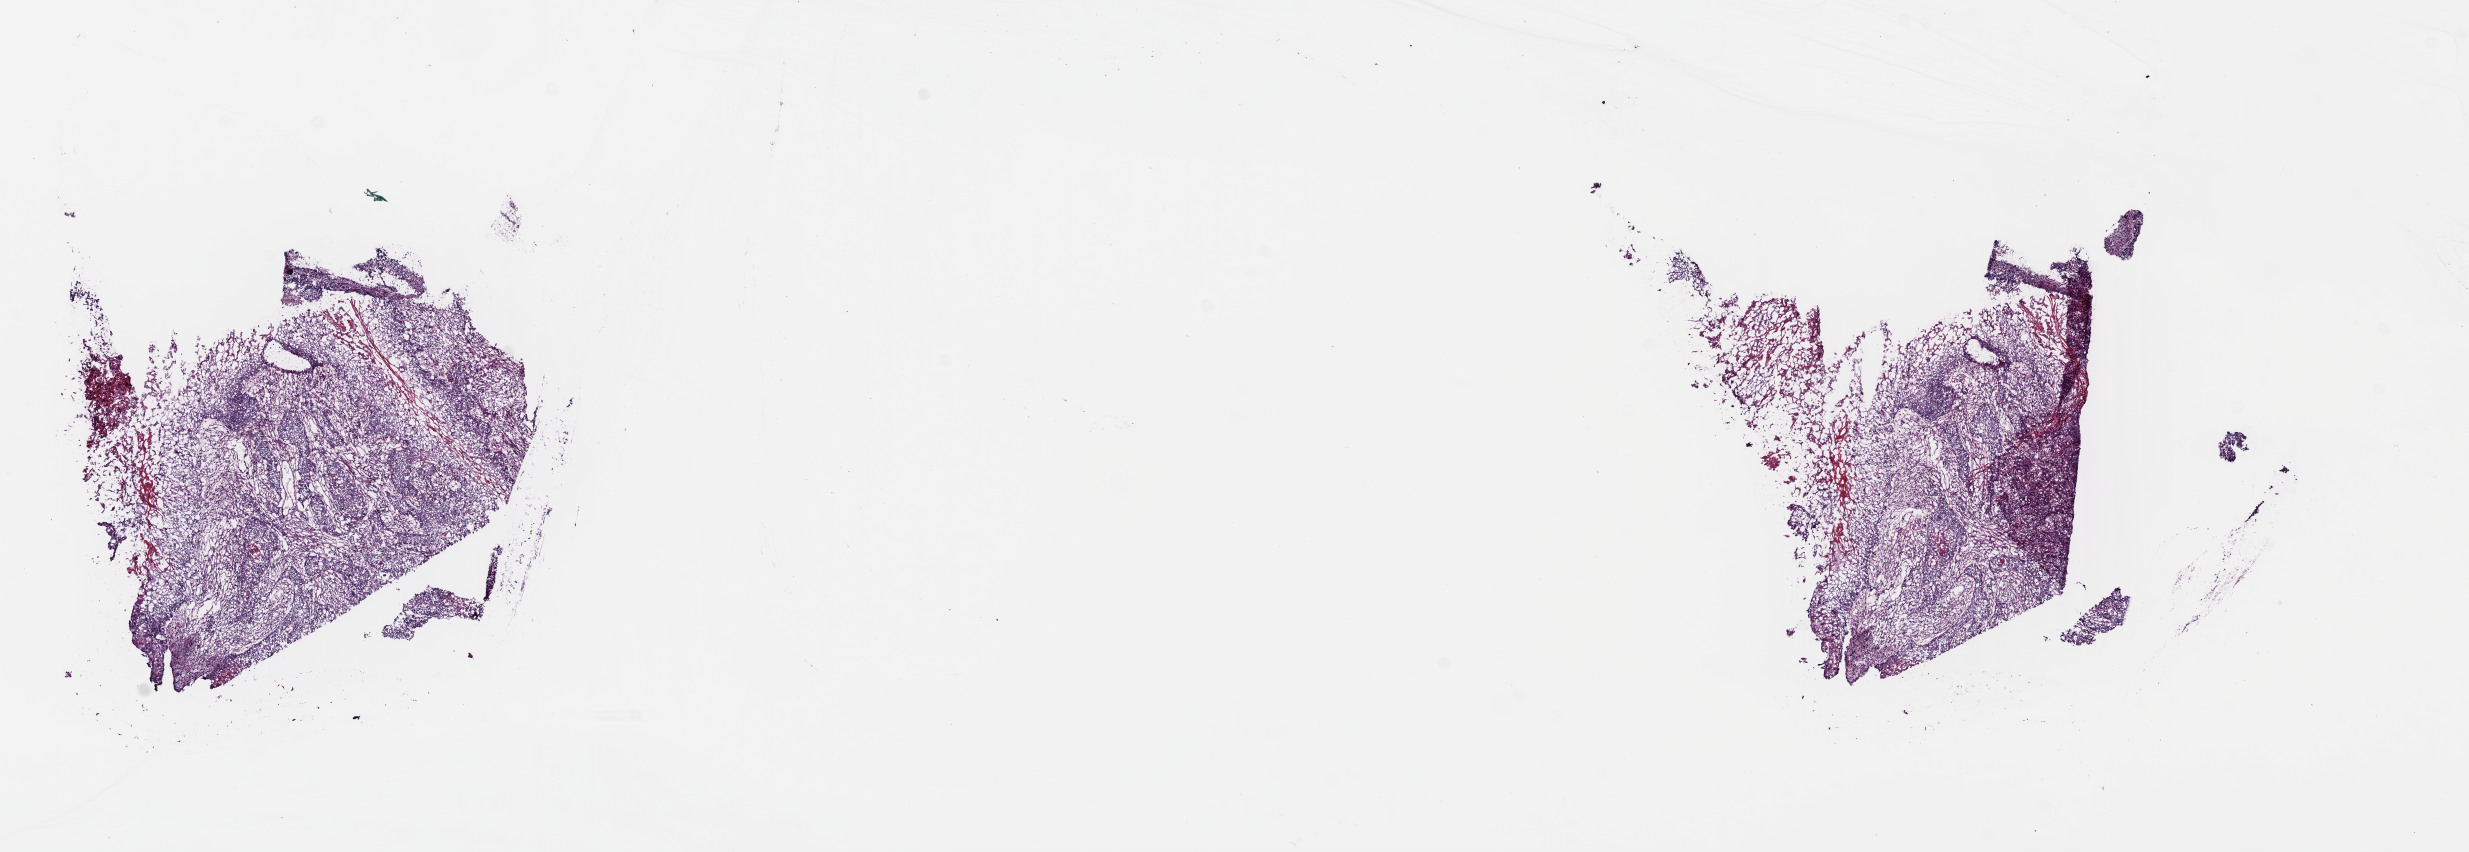
Digitized H&E tissue section (whole slide) — shown as a low-resolution overview of the whole scanned area (about 19.4 x 6.7 mm, from a 40x scan); frozen section from the top of the tissue portion; primary tumour sample from the lung. Male, age 74 years at initial diagnosis.
Pathologic diagnosis: Squamous cell carcinoma, NOS (upper lobe, lung).